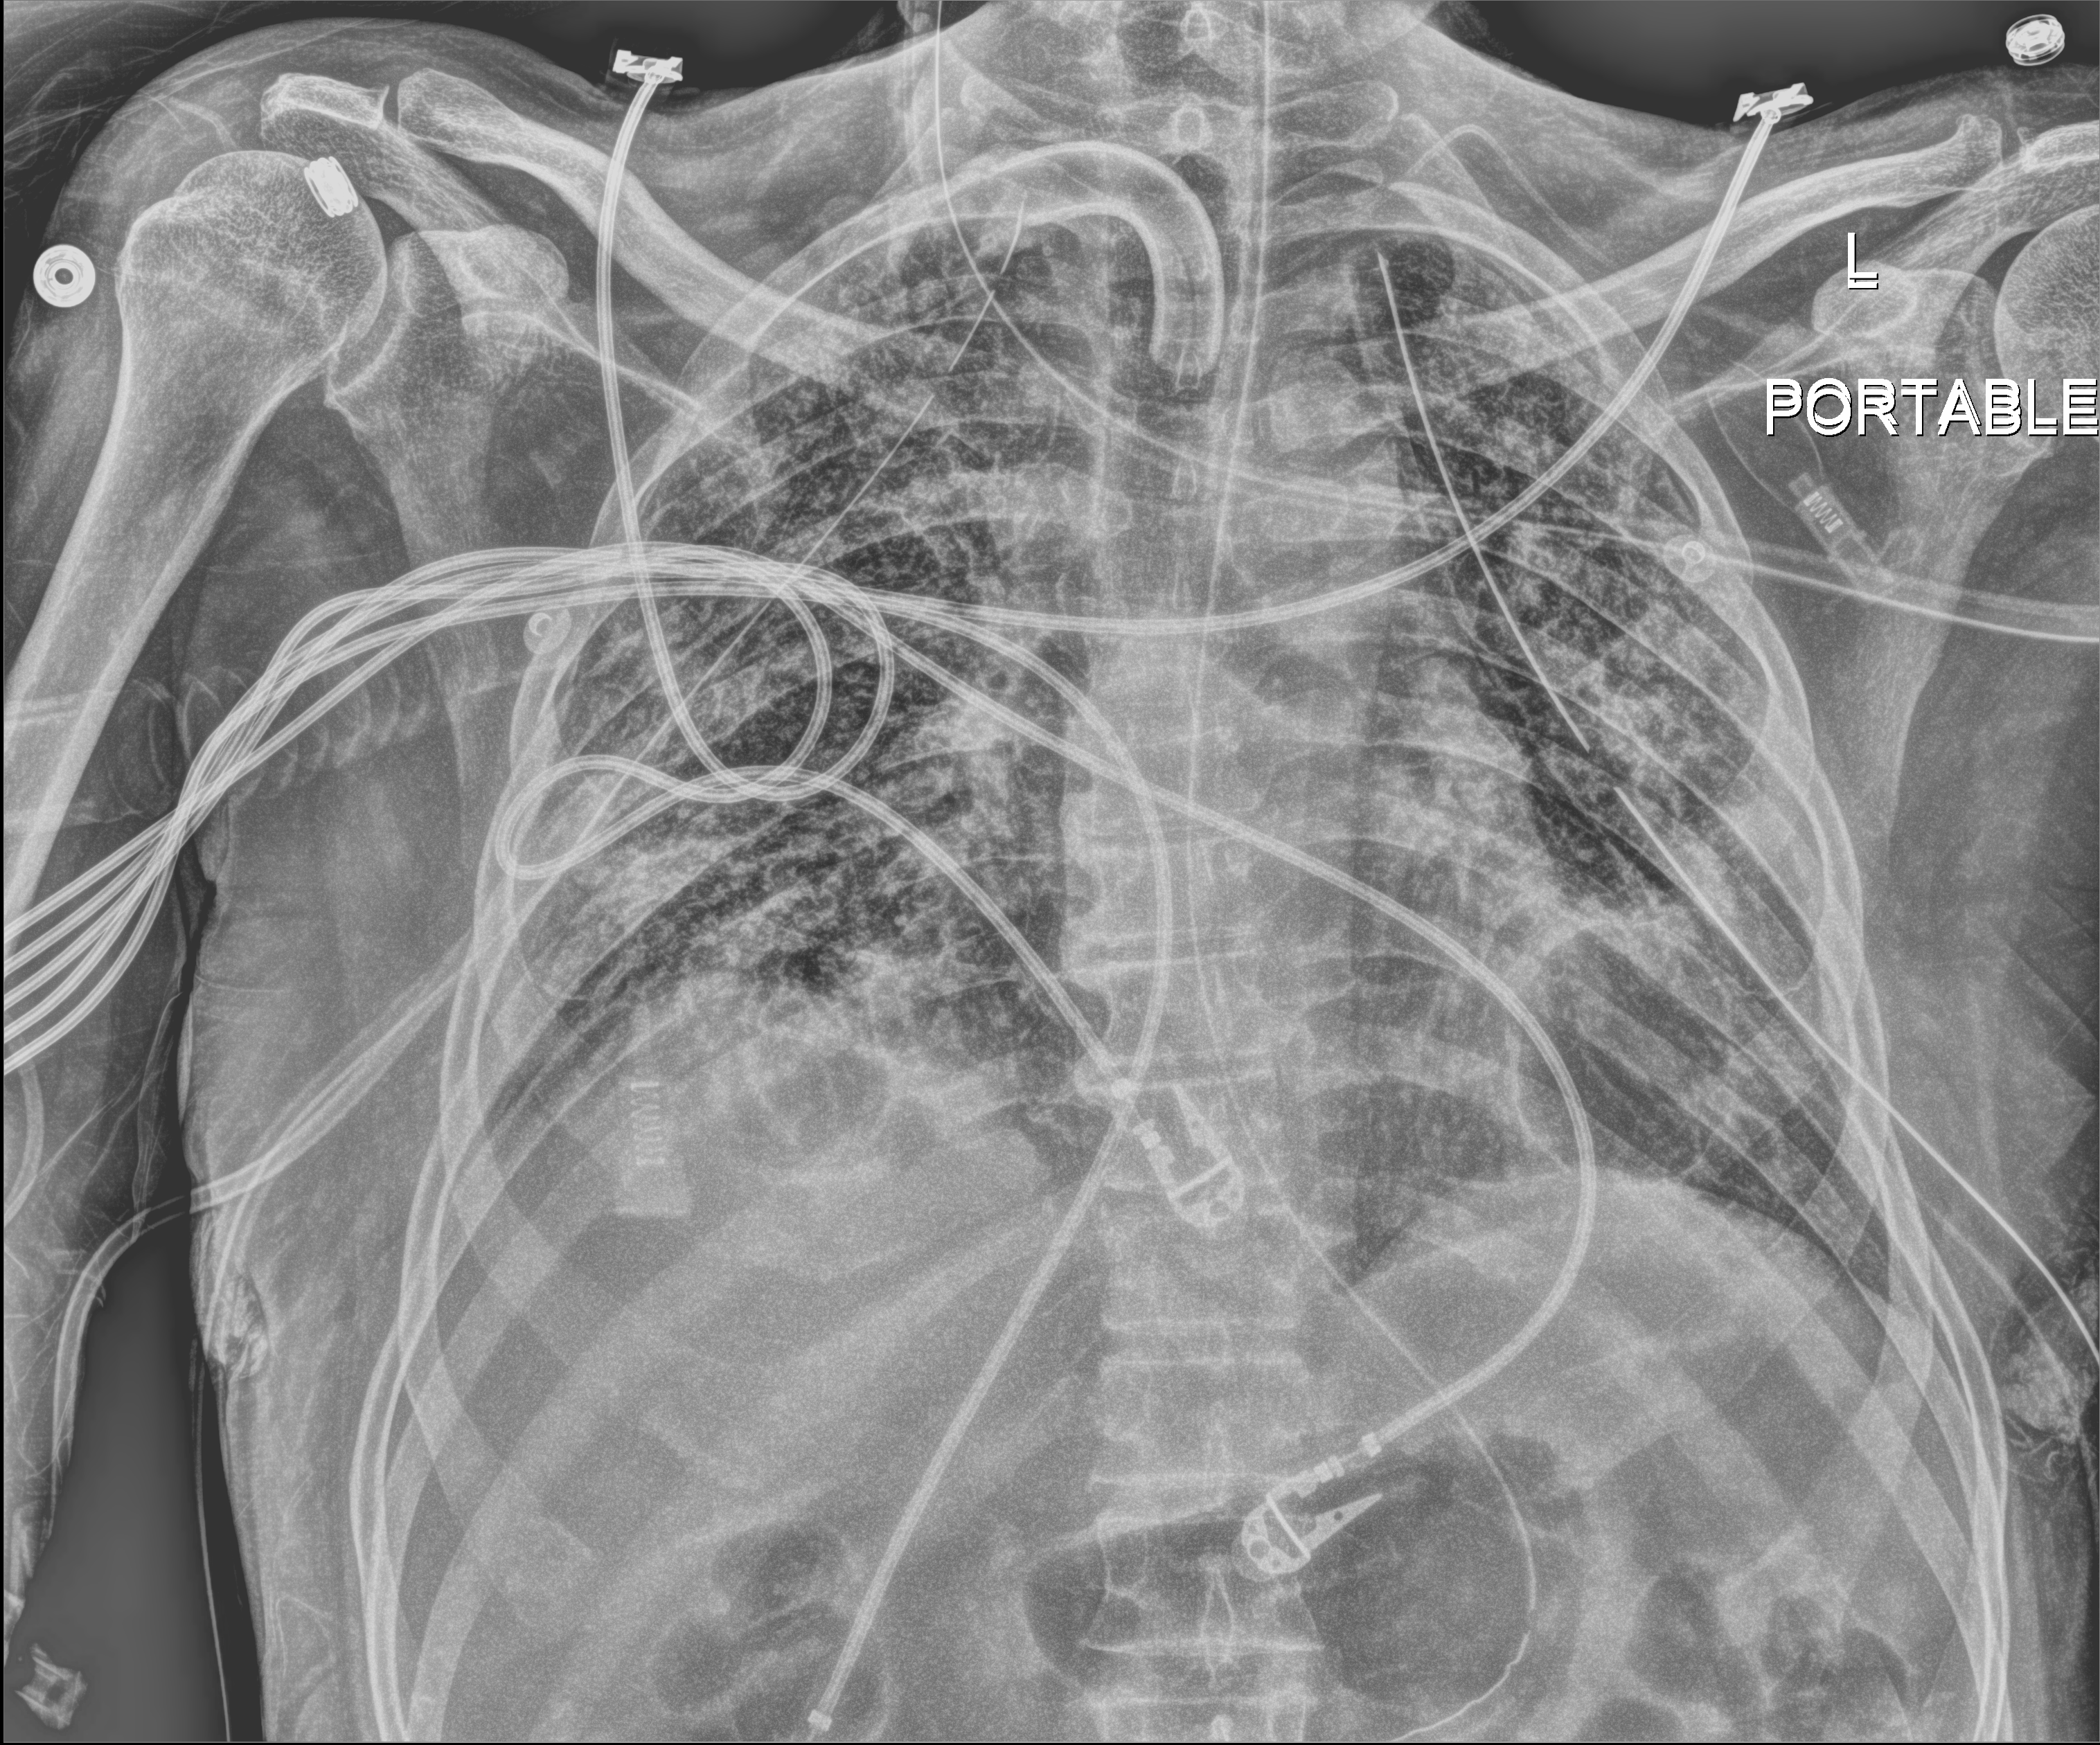
Portable chest radiograph; anteroposterior (AP) projection. Patient hospitalised with COVID-19; male, aged 18–59 years.
From the hospital-stay record, not from the radiograph (when in the stay this image was taken is not recorded): hypertension (admission record): yes; other chronic lung disease (admission record): no; admitted to intensive care during this hospital stay: yes.